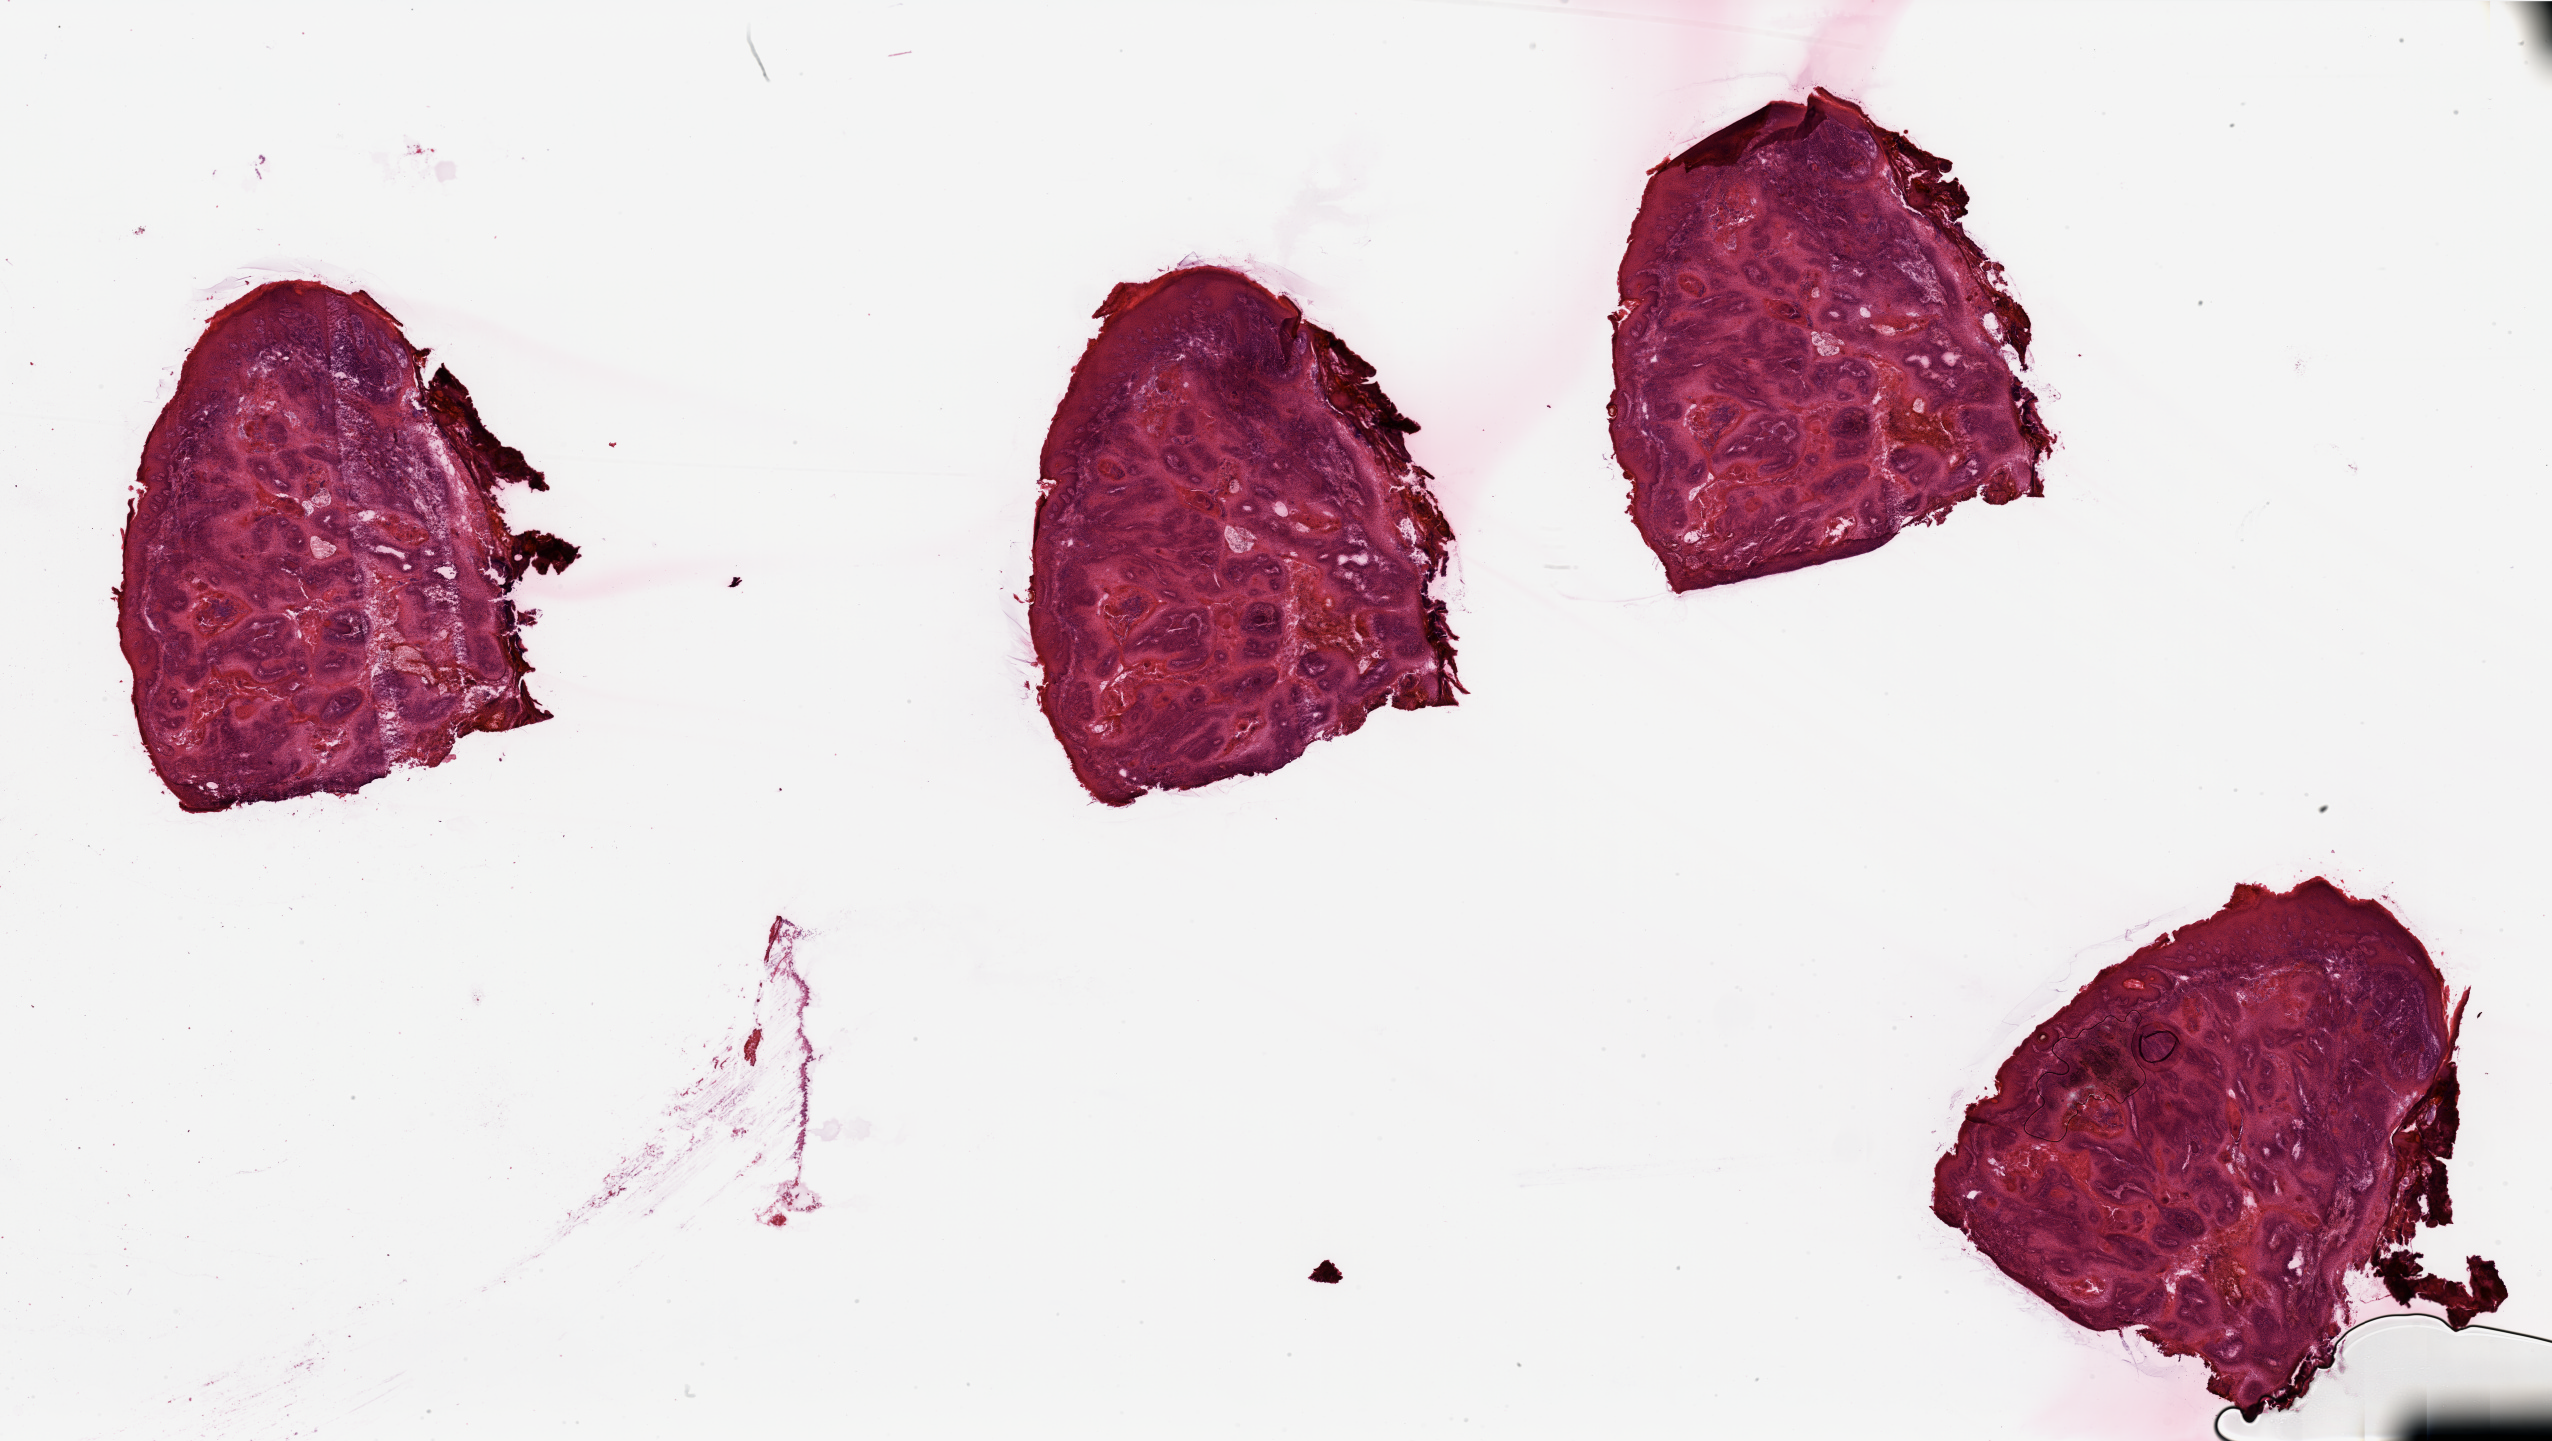
Hematoxylin and eosin (H&E) stained whole-slide image, a low-resolution overview of the entire scanned area, about 40.4 x 22.8 mm (acquisition: 20x scan), head and neck, tissue type not recorded. 54-year-old male patient.
- patient diagnosis: Squamous cell carcinoma, NOS (lip, NOS)